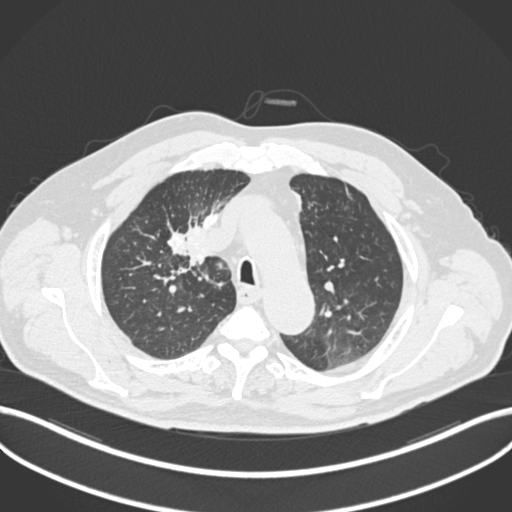
Chest CT, one axial slice; slice 150 of 255 in the series (ordered by position); lung window (W 1500 / L -600 HU); 512 × 512 image matrix, field of view 400 × 400 mm. Male patient, age 60 years. Case-level facts recorded for this patient, not image findings: clinical TNM (as recorded): T1b N1 M0.
Structures marked on this image (rectangle marked by the reading radiologist):
- lung tumour (recorded histology: squamous cell carcinoma): bounding box <162,225,210,275> (left, top, right, bottom; pixels)